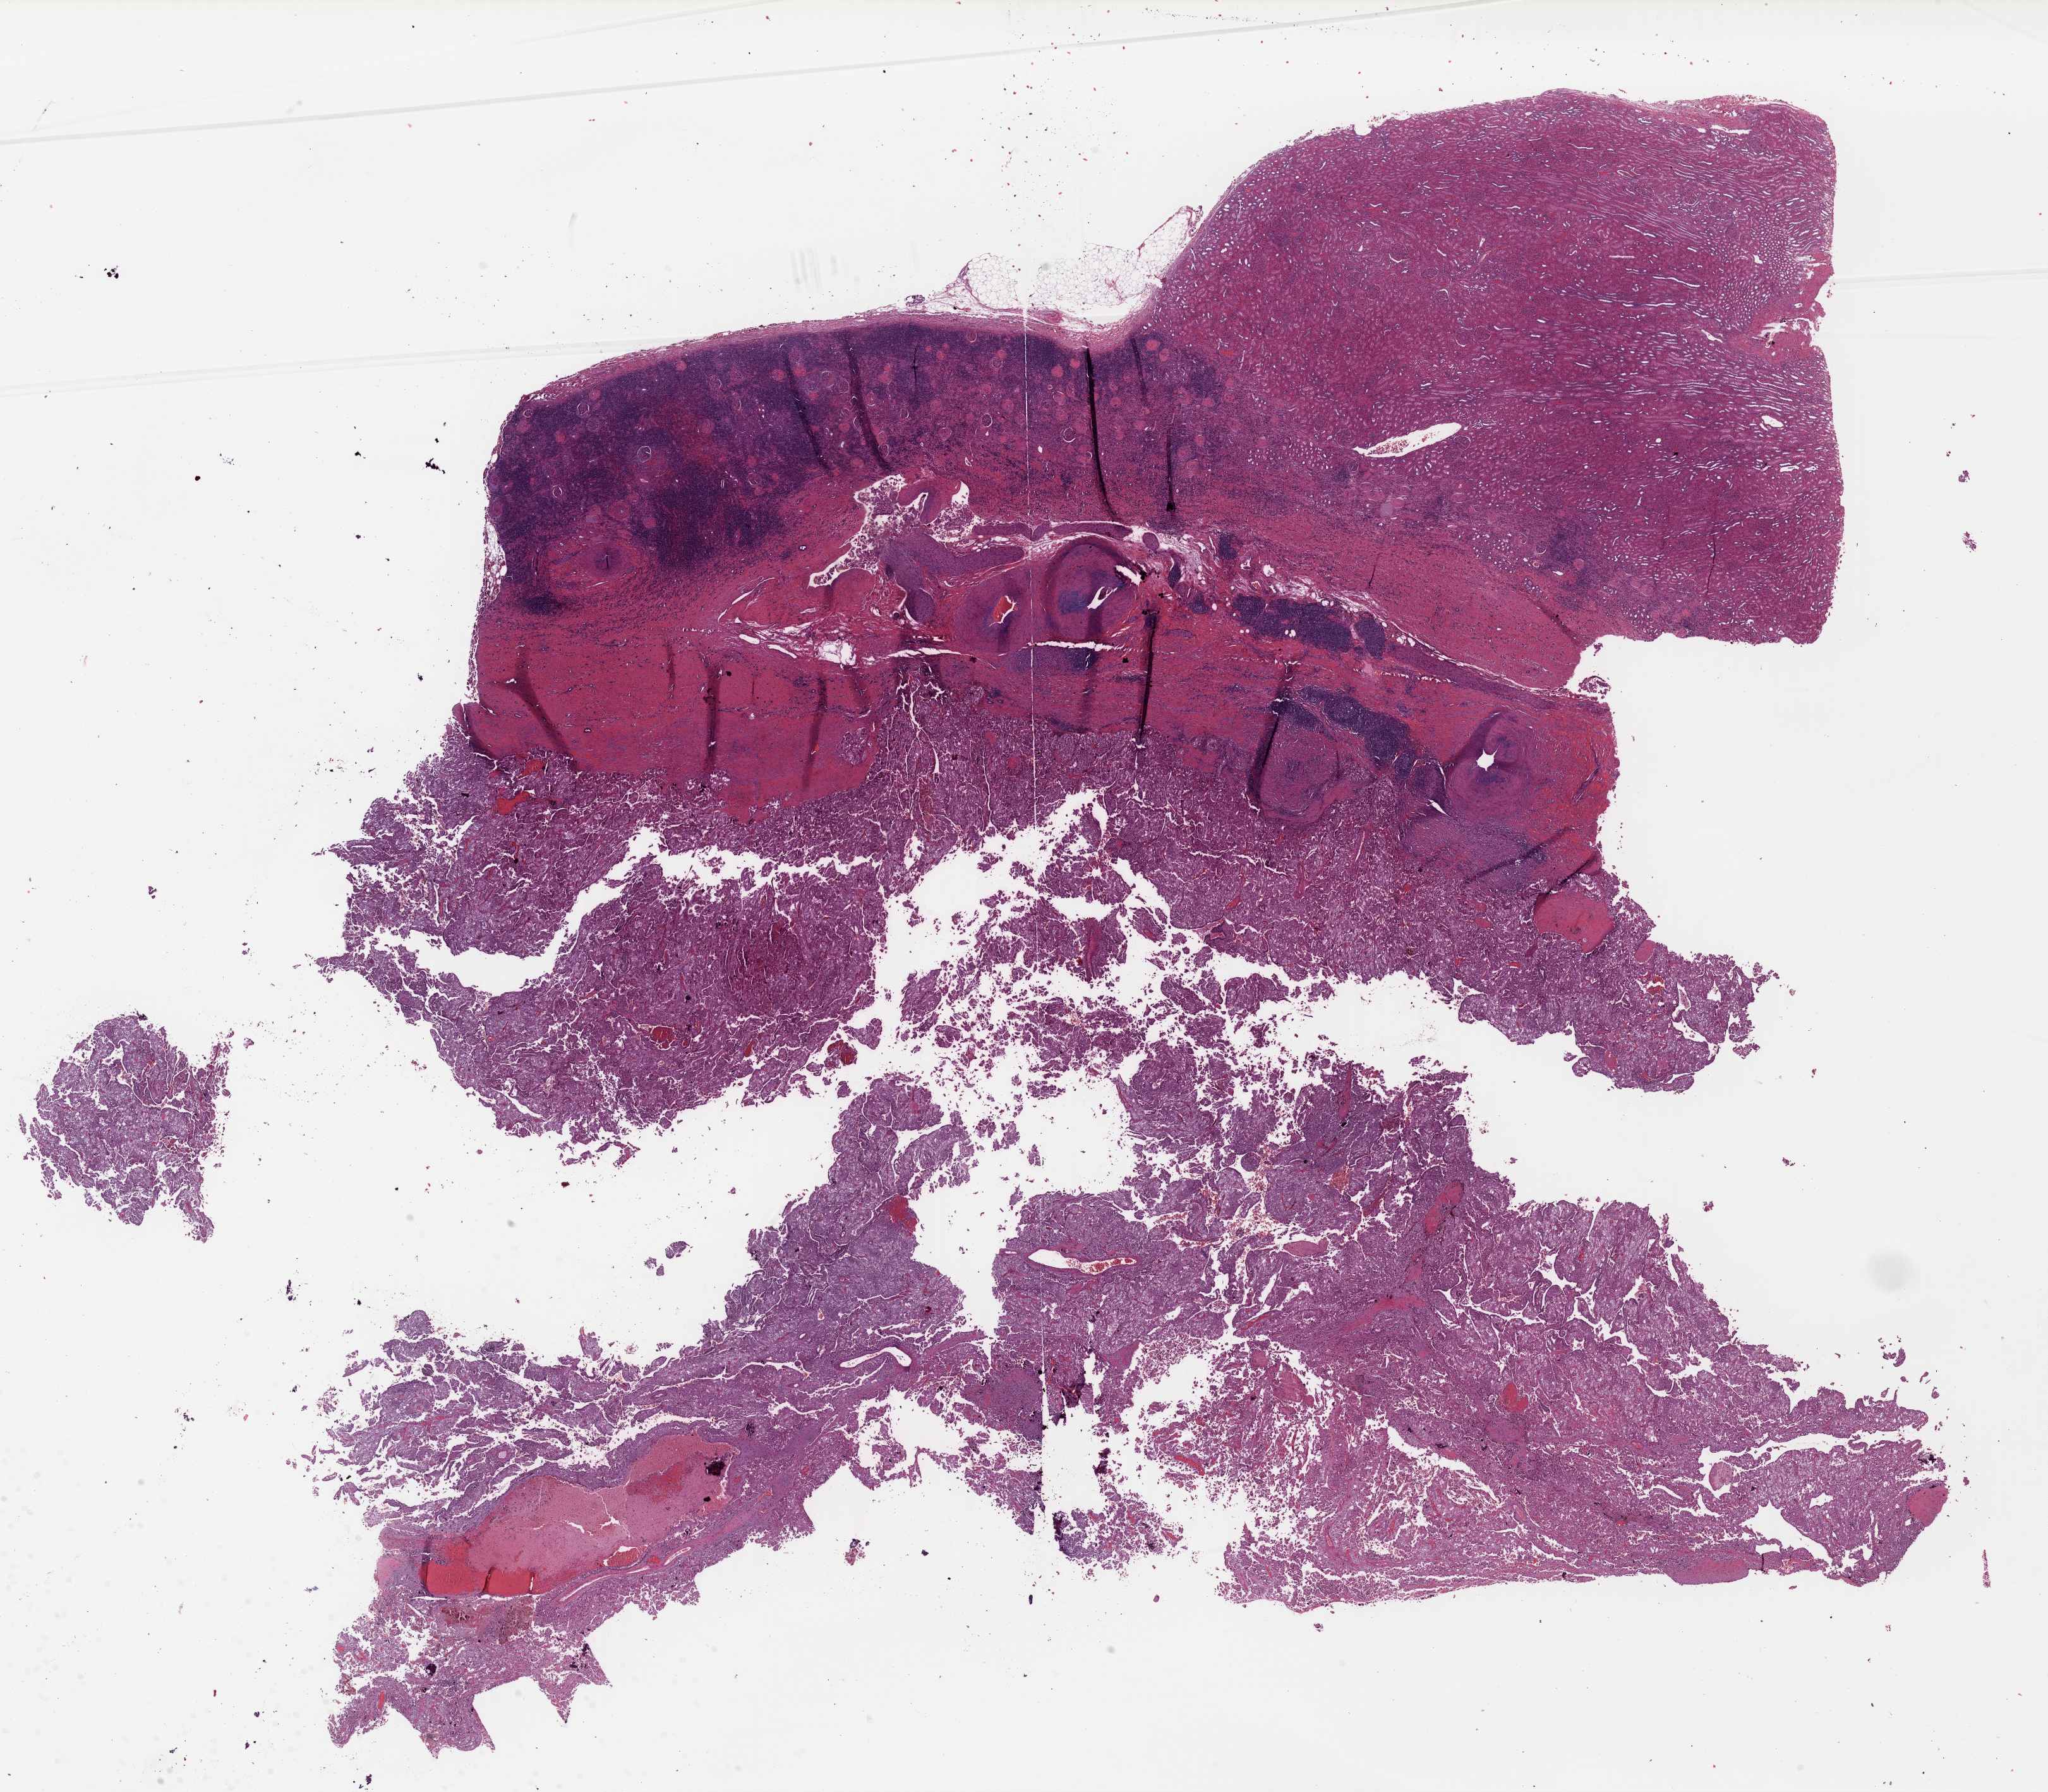
Digitized Hematoxylin and eosin (H&E) stained tissue section (whole slide) — a low-resolution overview of the entire scanned area, about 25.5 x 22.3 mm, formalin-fixed paraffin-embedded (FFPE) diagnostic section, sample: primary tumour, kidney. Patient: male, age at initial diagnosis 41 years.
Diagnosis: Renal cell carcinoma, chromophobe type.